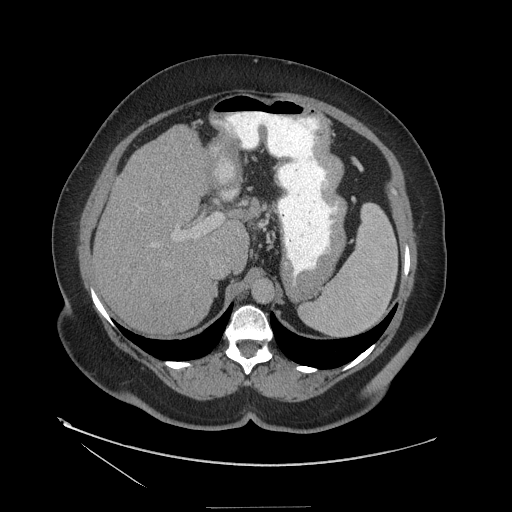
Contrast-enhanced abdominal CT (liver protocol), one axial slice; slice 78 of 127 in the series (ordered by position); reconstruction kernel STANDARD; 140 kVp; soft-tissue window (W 400 / L 40 HU); 2.5 mm slice thickness; 512 × 512 image matrix, field of view 480 × 480 mm. Case-level facts recorded for this patient, not image findings: diagnosis: hepatocellular carcinoma (patient treated with transarterial chemoembolisation; whether this scan precedes or follows treatment is not stated here); TNM stage (as recorded): Stage-II; Child-Pugh class: A; tumour differentiation: well differentiated; tumour nodularity: multinodular.
Annotated regions visible in this slice (semi-automatic segmentation, software-assisted and operator-edited):
- liver parenchyma outside the tumour (the mass and vessels are separate outlines, so this box may not span the whole liver): bounding box <93,114,266,334> (left, top, right, bottom; pixels)
- liver vessels: <173,114,267,238>